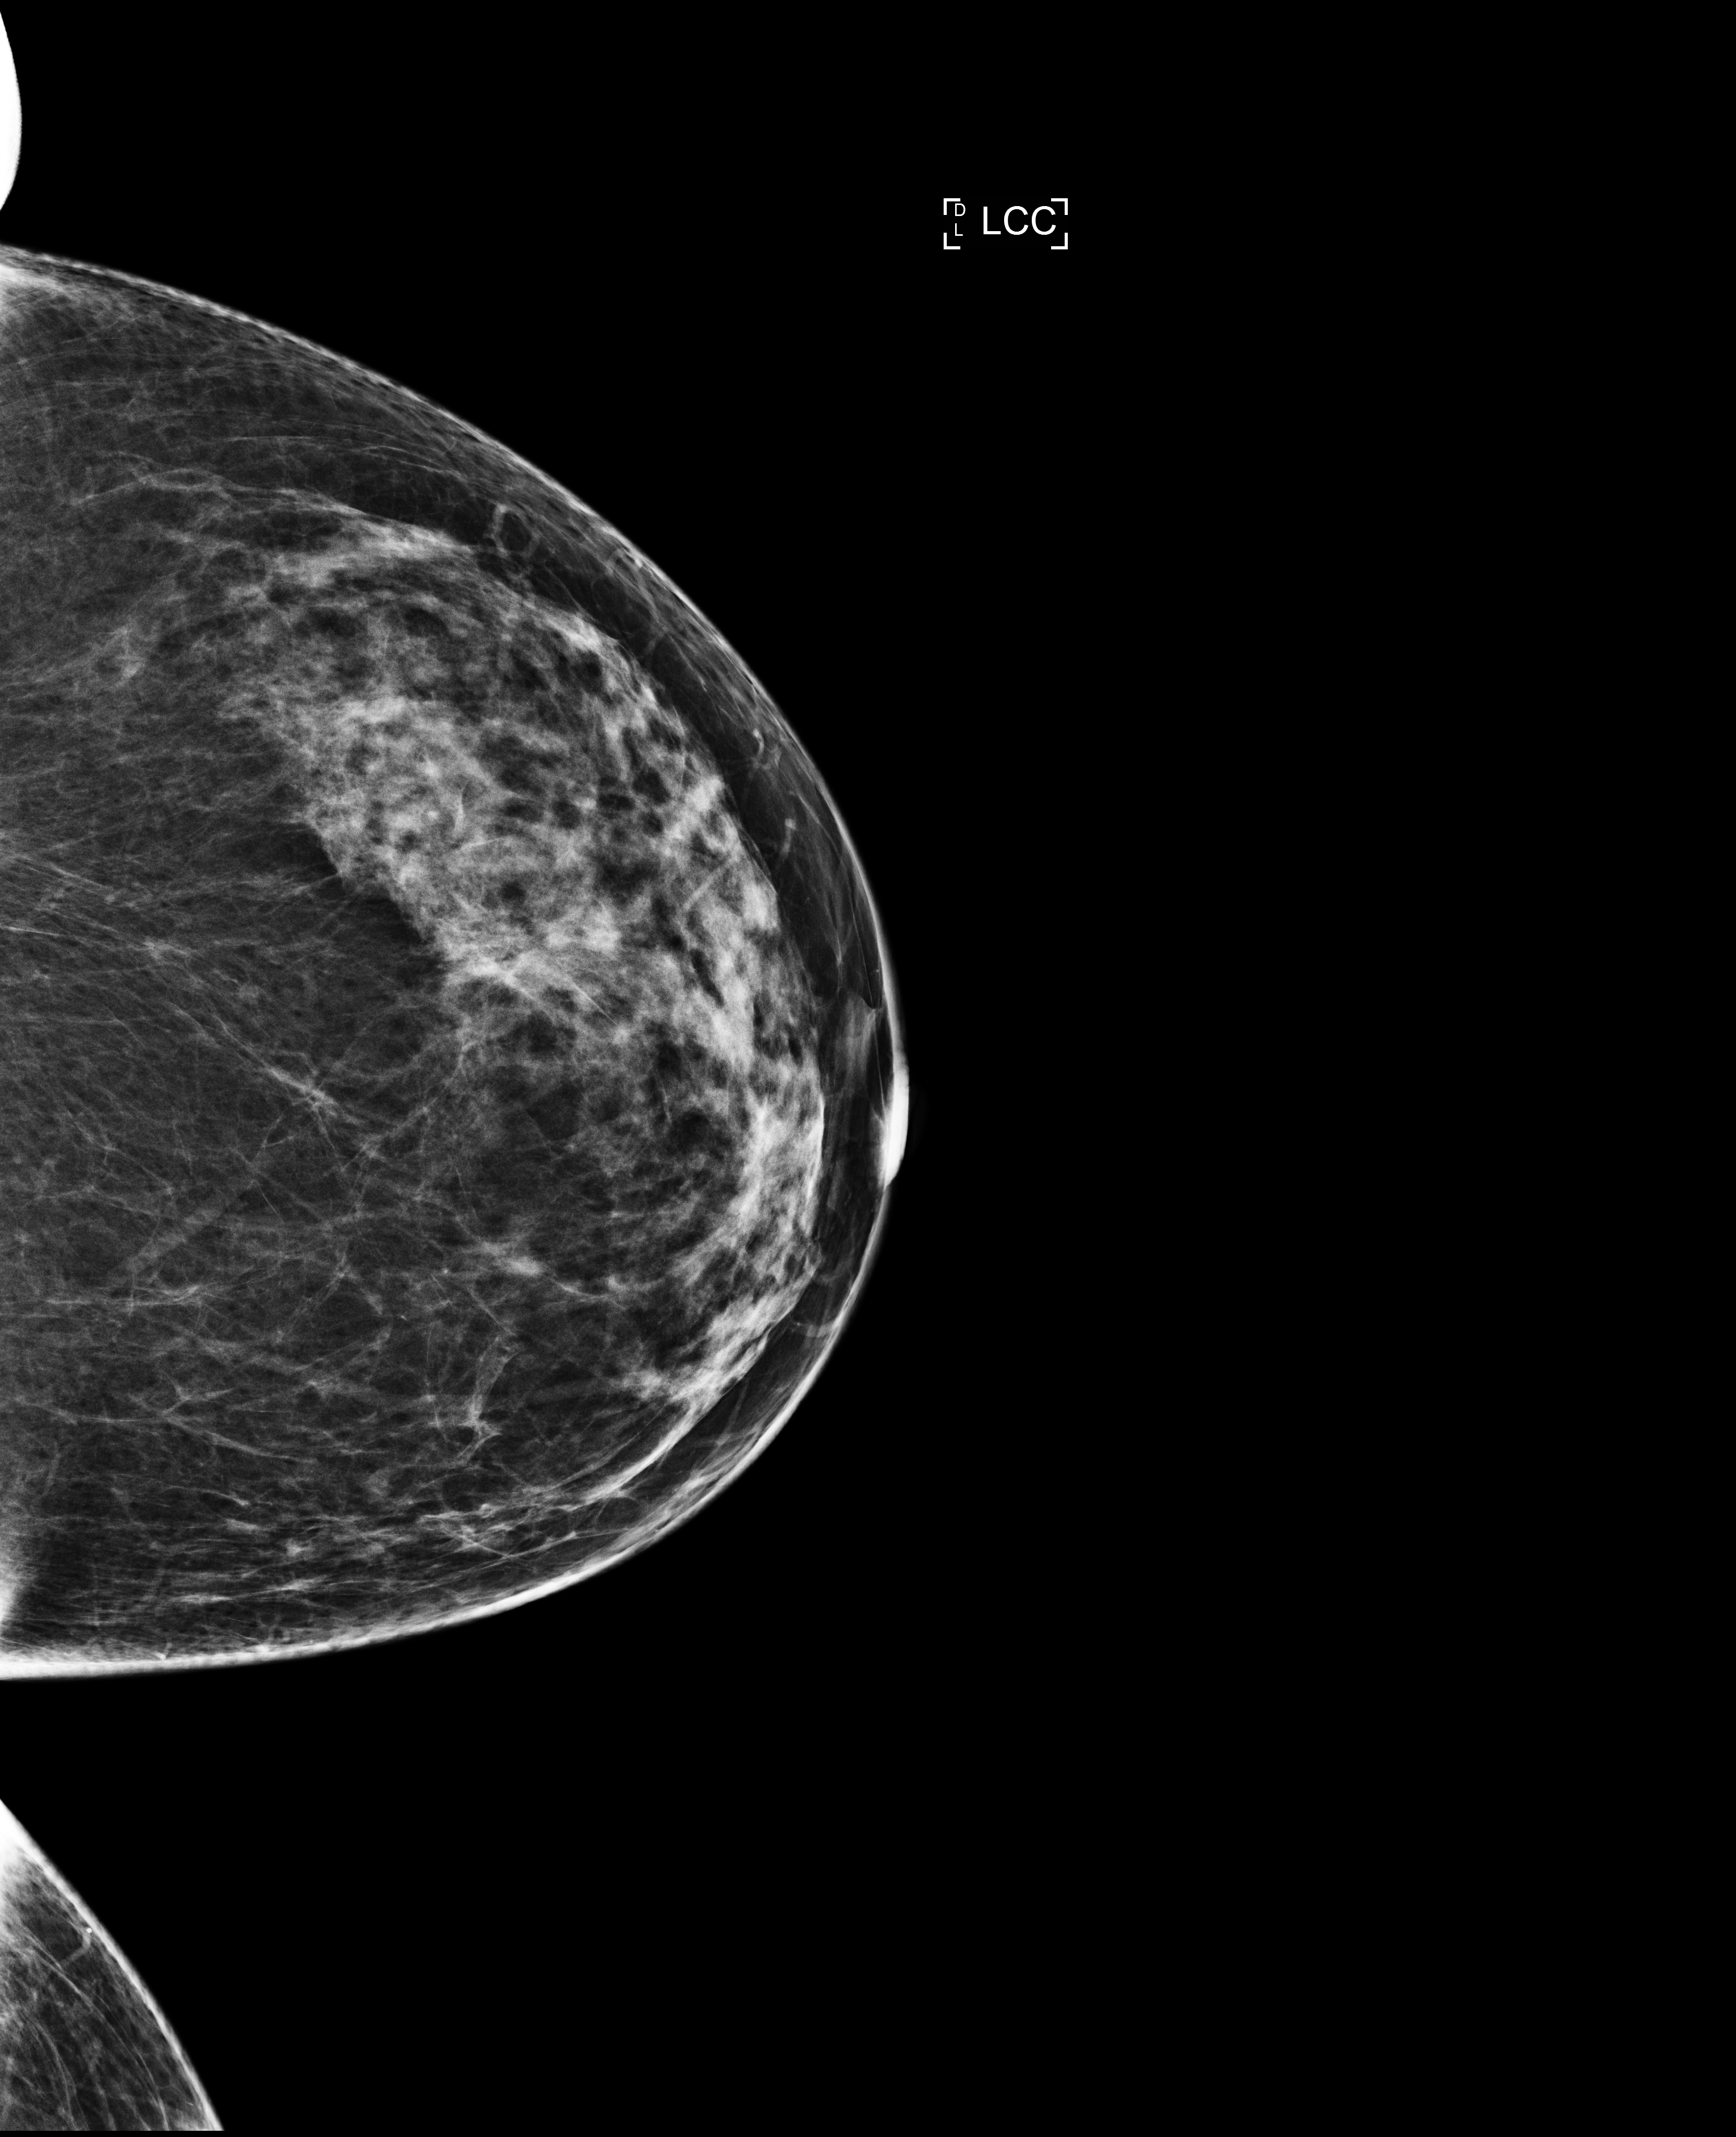
Screening examination. Female patient, age 47 years.
Image type: full-field digital mammogram. Breast: left. Projection: CC view.